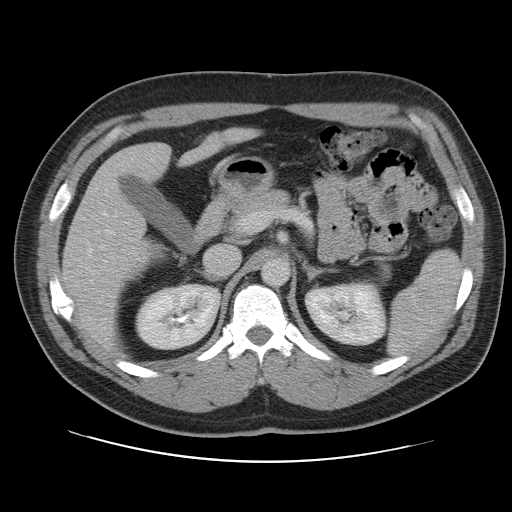
Contrast-enhanced abdominal CT, one axial slice; position 63 of 109 along the scan axis; 120 kVp; intravenous contrast given; soft-tissue window (W 400 / L 40 HU); 5 mm slice thickness; 512 × 512 image matrix, field of view 402 × 402 mm. Male patient, age 35 years. Case-level facts recorded for this patient, not image findings: diagnosis: colorectal cancer liver metastases, imaged before liver resection; multiple liver metastases: yes; largest metastasis: 2.8 cm.
Annotated regions visible in this slice (expert manual segmentation):
- liver: bounding box [x1, y1, x2, y2] px = [63, 130, 249, 350]
- planned liver remnant (the part of the liver to remain after resection): [63, 130, 250, 350]
- portal vein (with intrahepatic branches): [84, 210, 118, 284]